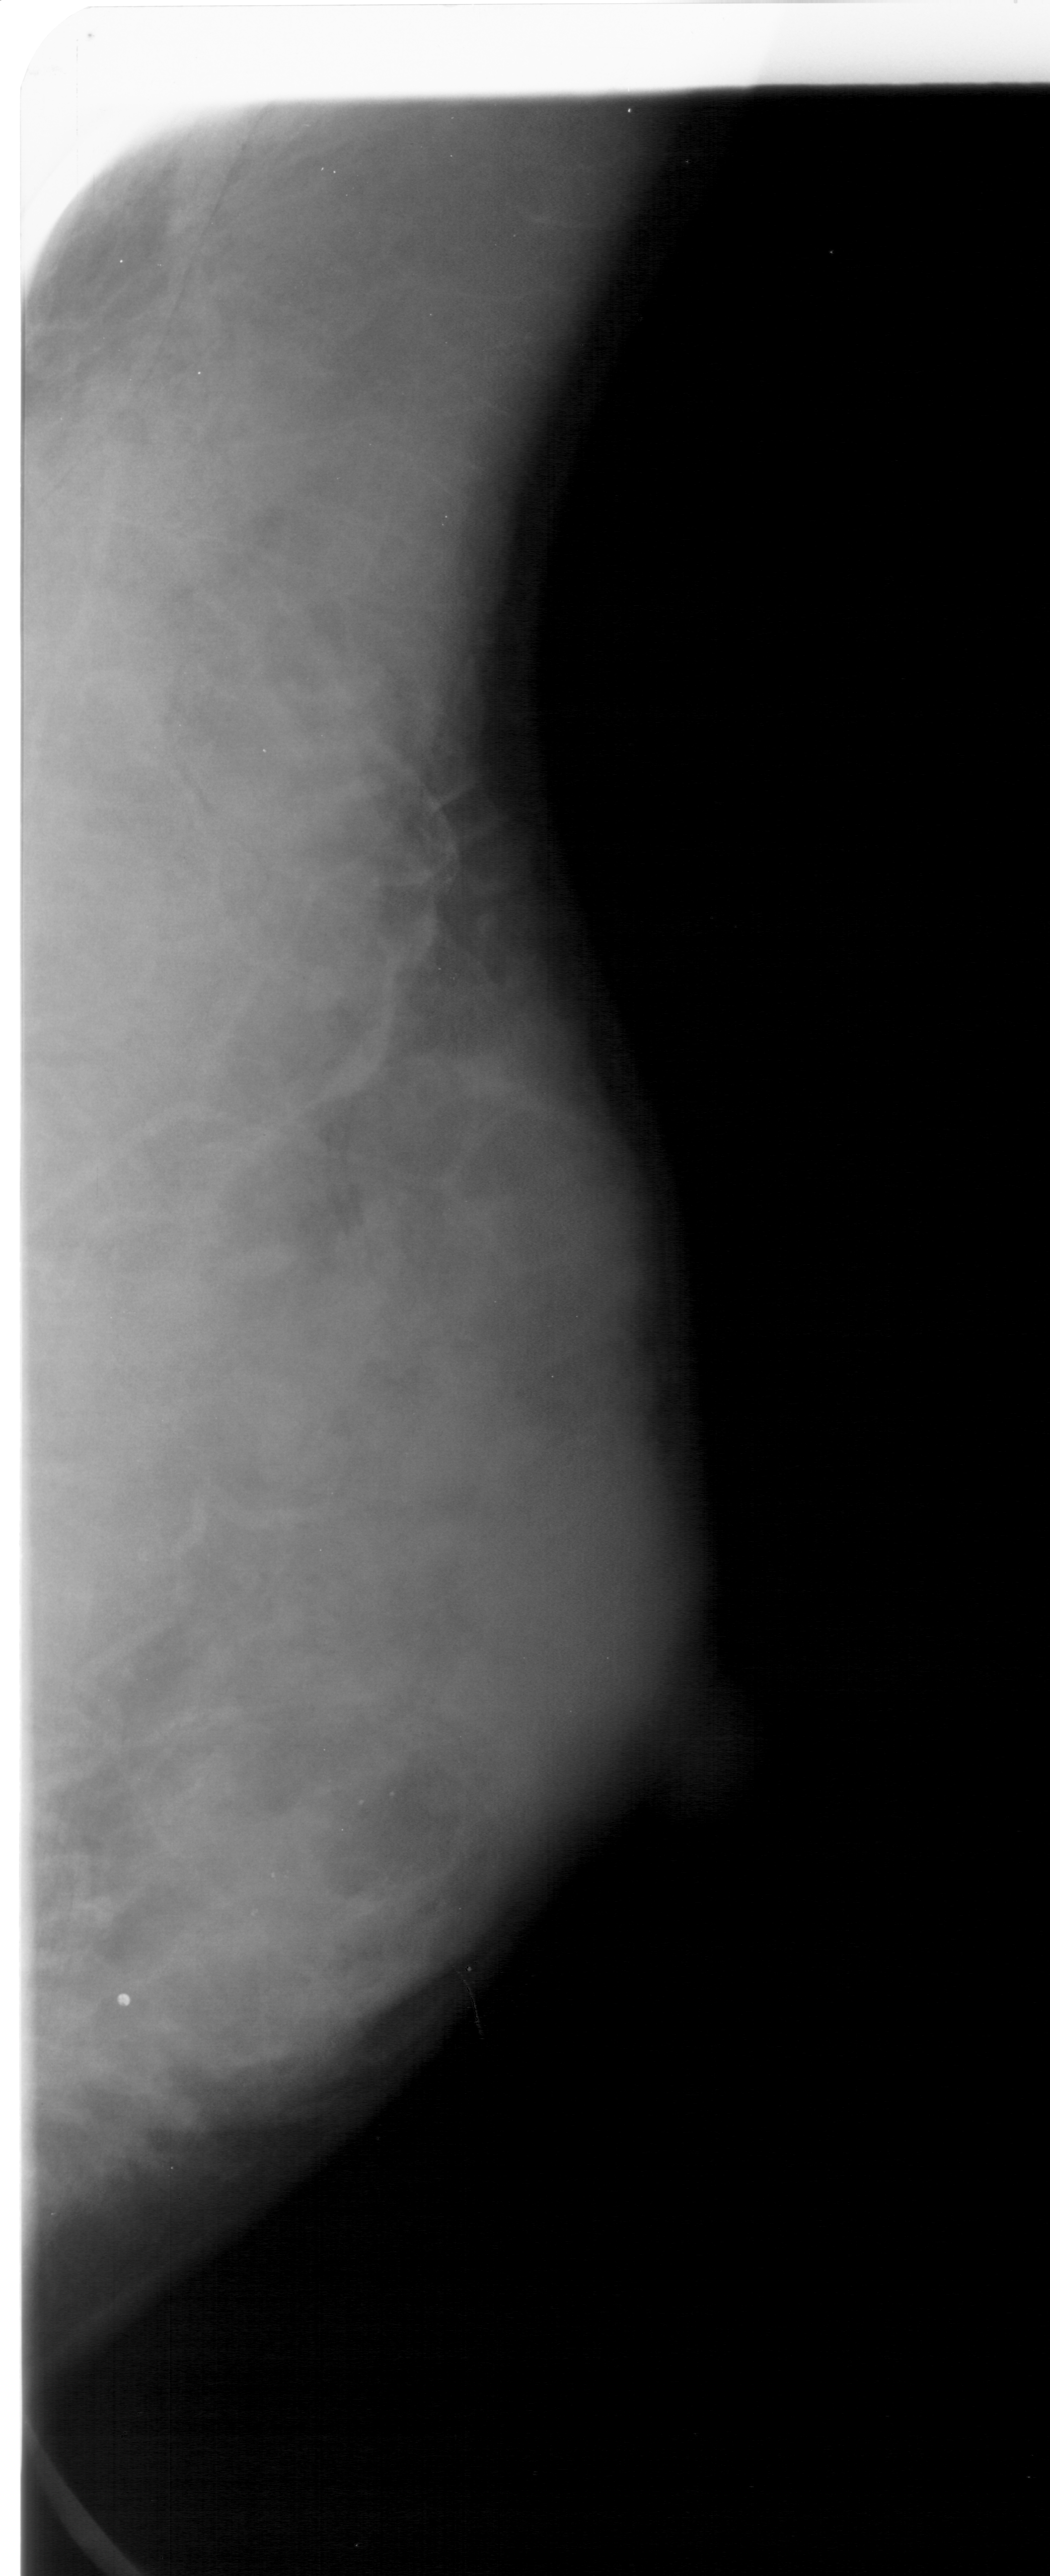
Scanned film-screen mammogram. Right breast. Mediolateral oblique (MLO) view. Breast composition: extremely dense (BI-RADS density category 4 of 4). 1050 × 2576 image matrix.
Marked abnormalities (boxes around the expert regions of interest):
- calcifications, morphology pleomorphic, distribution segmental; BI-RADS assessment category 4; pathology result (as recorded, not read from the image): benign: bounding box <235,1758,426,1941> (left, top, right, bottom; pixels)